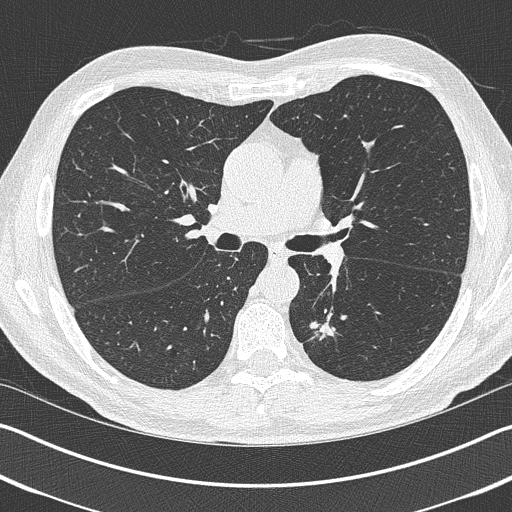
Axial slice from a low-dose chest CT screening exam; baseline screening round; lung window (W 1500 / L -600 HU); slice 157 of 402 in the series; 512 × 512 image matrix. Male participant, aged 69 years at enrolment. Current smoker at enrolment.
Expert reader's lesion annotation, bounding box <302,309,356,360> (left, top, right, bottom; pixels). Screening reader's record for this exam (one nodule recorded; not confirmed to be the boxed lesion): non-calcified nodule or mass ≥4 mm, left upper lobe, 19 × 19 mm, spiculated (stellate) margins, pre-existing on the prior screen: yes. Later outcome: lung cancer diagnosed 202 days after this screen — non-small cell carcinoma, left lower lobe, stage IIIA (AJCC 6th edition), 20 mm at pathology.